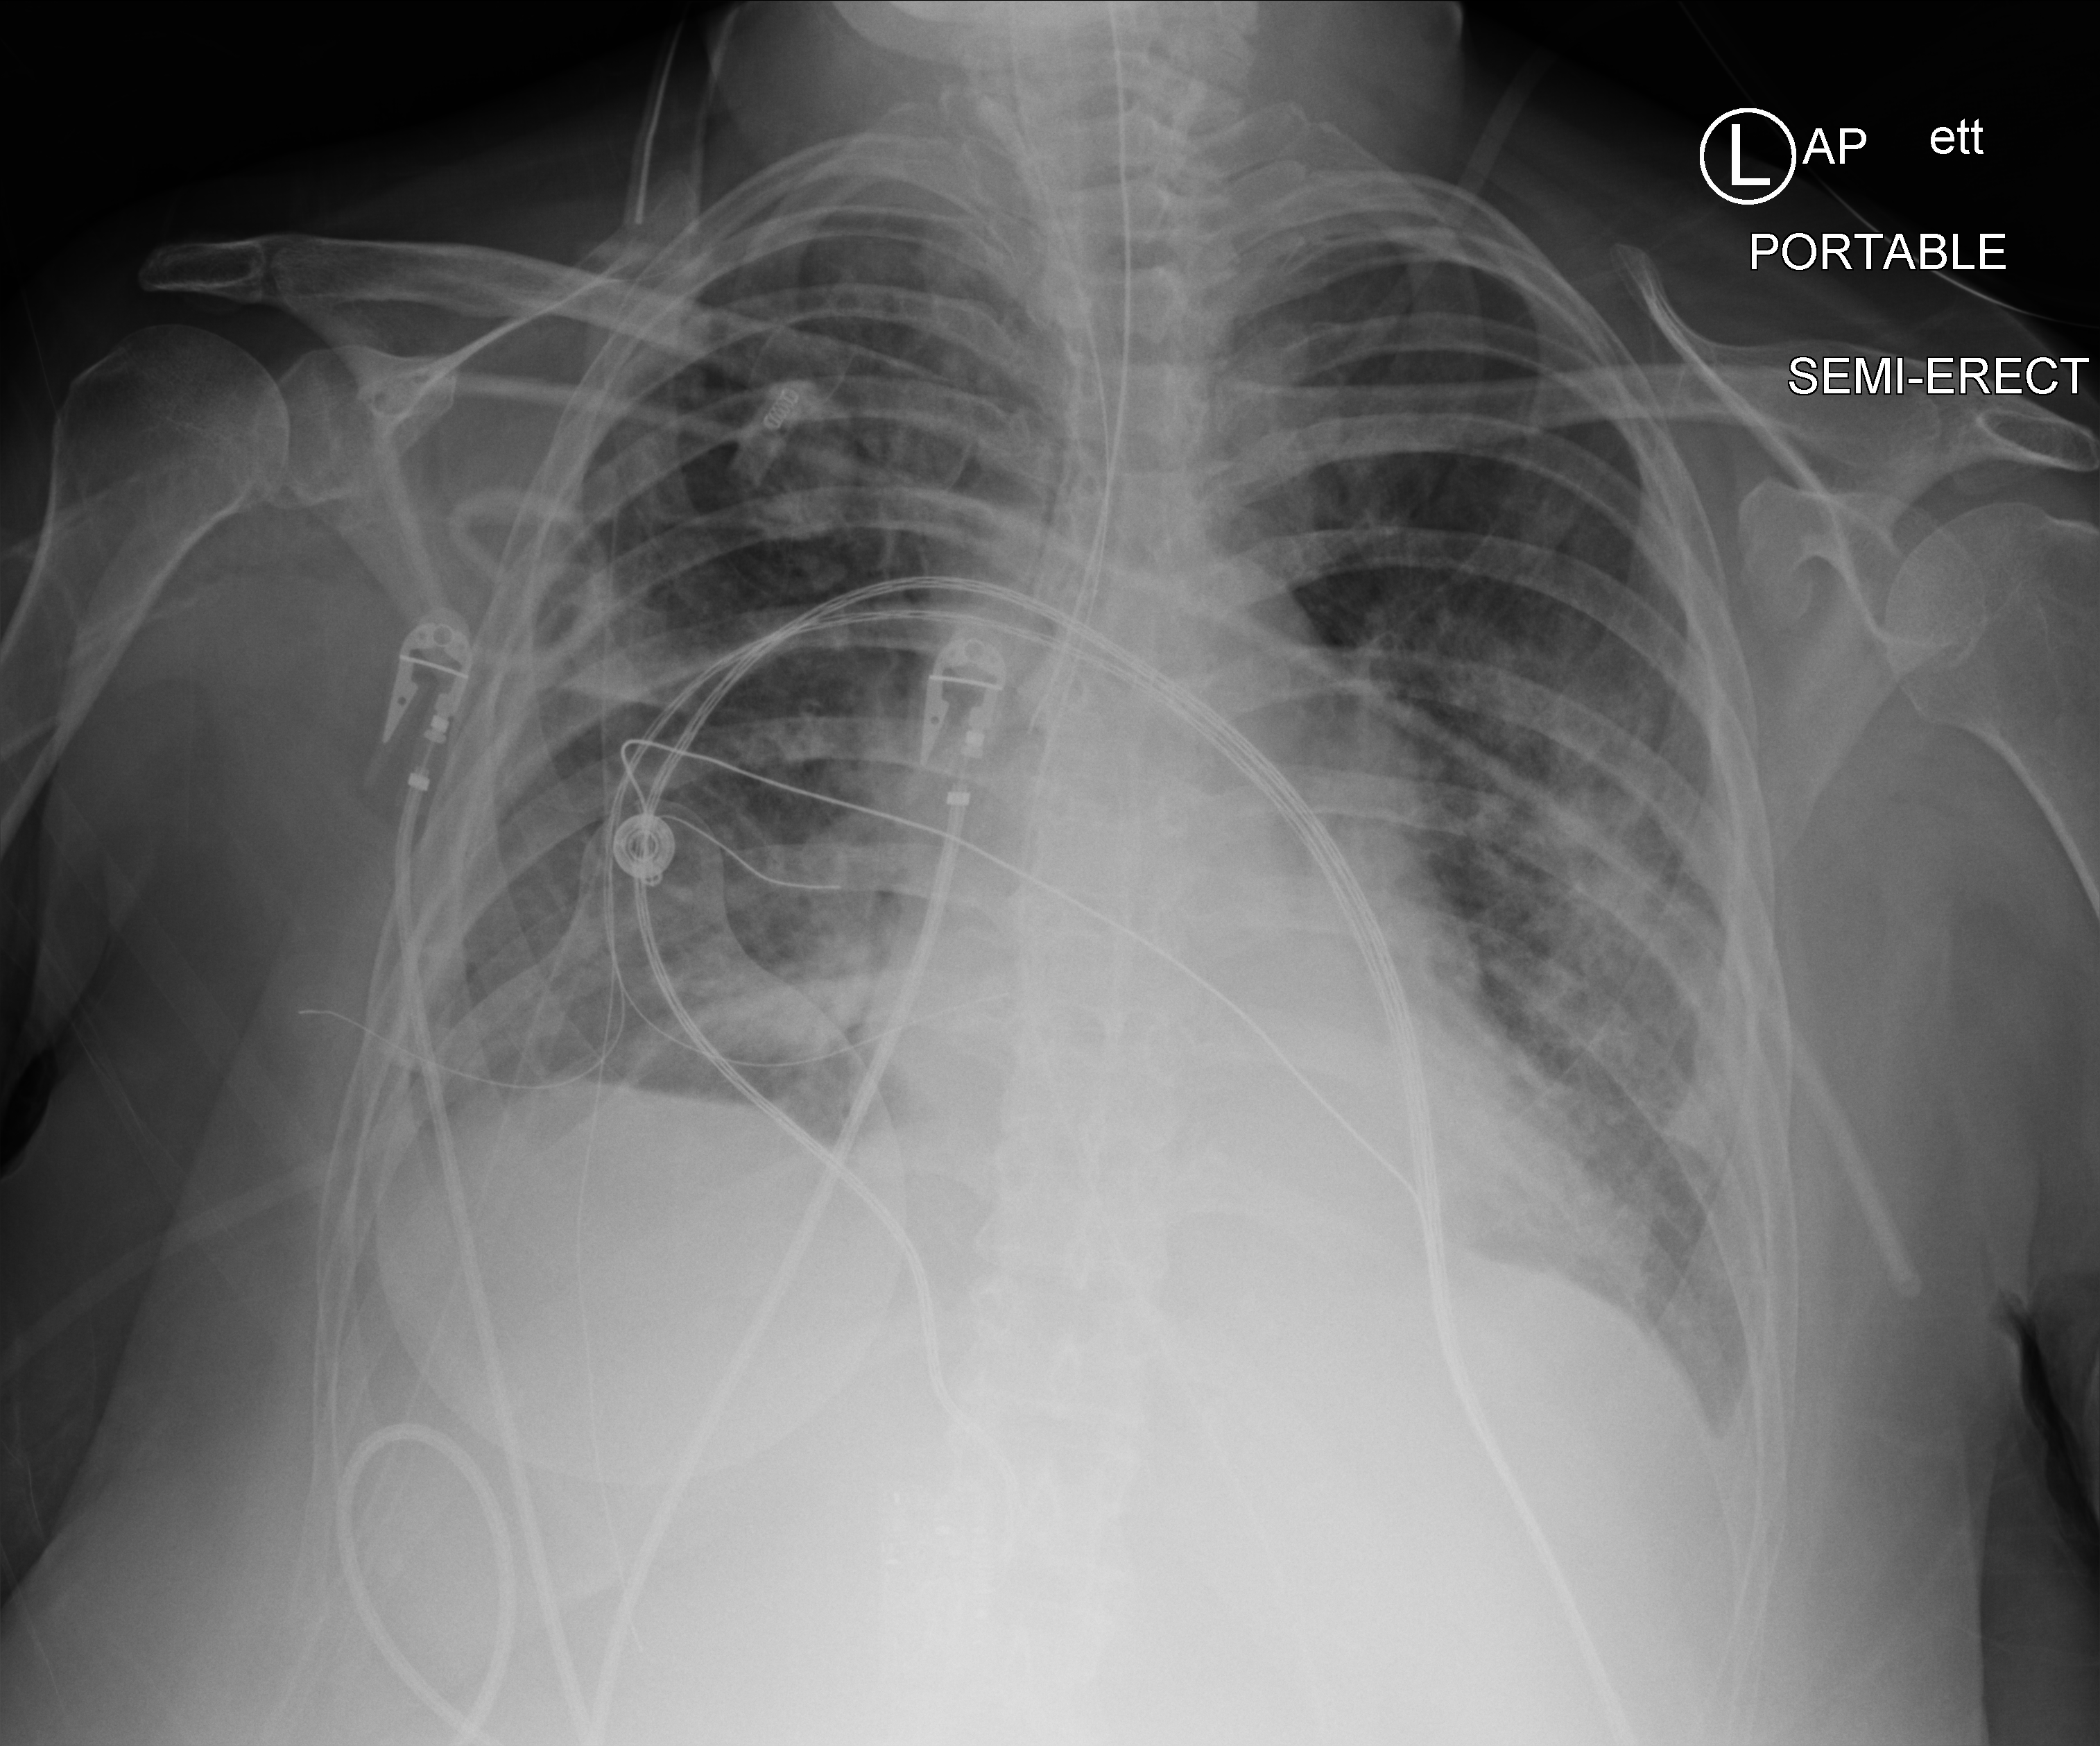
Bedside chest radiograph (computed radiography), anteroposterior (AP) projection. Patient hospitalised with COVID-19; female, aged 60–74 years.
From the hospital-stay record, not from the radiograph (when in the stay this image was taken is not recorded): length of hospital stay: 9 days; mechanically ventilated during this hospital stay: yes; admitted to intensive care during this hospital stay: yes.